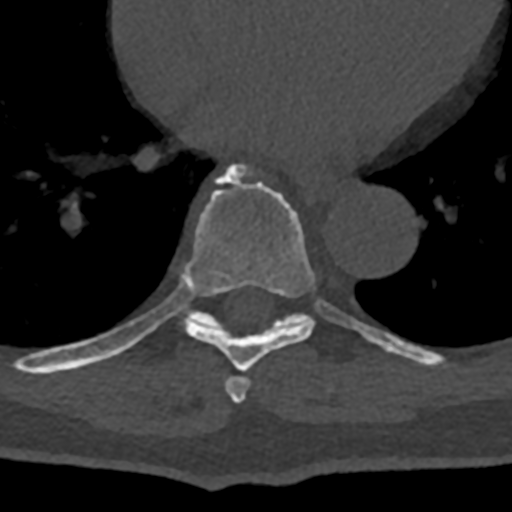
CT including the spine, one axial slice. Slice 698 of 797 in the series (ordered by position). Reconstruction kernel Br40s/3. 120 kVp. Bone window (W 1800 / L 400 HU). 0.5 mm slice thickness. 512 × 512 image matrix, field of view 160 × 160 mm. Male patient, age 74 years. From the clinical record (not read from this slice): primary cancer: renal.
Annotated regions visible in this slice (semi-automatic segmentation, software-assisted and operator-edited):
- T7 vertebra: box from (x=225, y=376) to (x=250, y=403) px
- T8 vertebra: (x=70, y=164)–(x=400, y=372)
- T9 vertebra: (x=172, y=283)–(x=432, y=366)